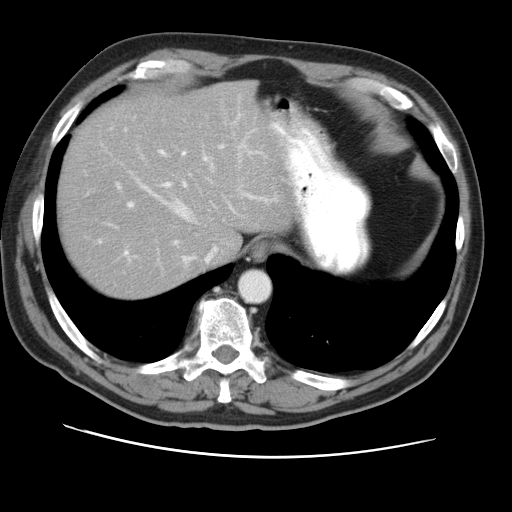
Contrast-enhanced abdominal CT, one axial slice. Slice 39 of 49 in the series (ordered by position). Reconstruction kernel STANDARD. Intravenous contrast given. Soft-tissue window (W 400 / L 40 HU). 5 mm slice thickness. 512 × 512 image matrix, field of view 374 × 374 mm. Male patient, age 59 years. From the clinical record (not read from this slice): diagnosis: colorectal cancer liver metastases, imaged before liver resection; multiple liver metastases: yes; largest metastasis: 6.3 cm; disease in both lobes: yes.
Annotated regions visible in this slice (manually delineated by an expert):
- hepatic veins: bounding box <142,141,259,264> (left, top, right, bottom; pixels)
- liver: <59,82,294,300>
- planned liver remnant (the part of the liver to remain after resection): <59,82,294,300>
- portal vein (with intrahepatic branches): <115,129,270,258>